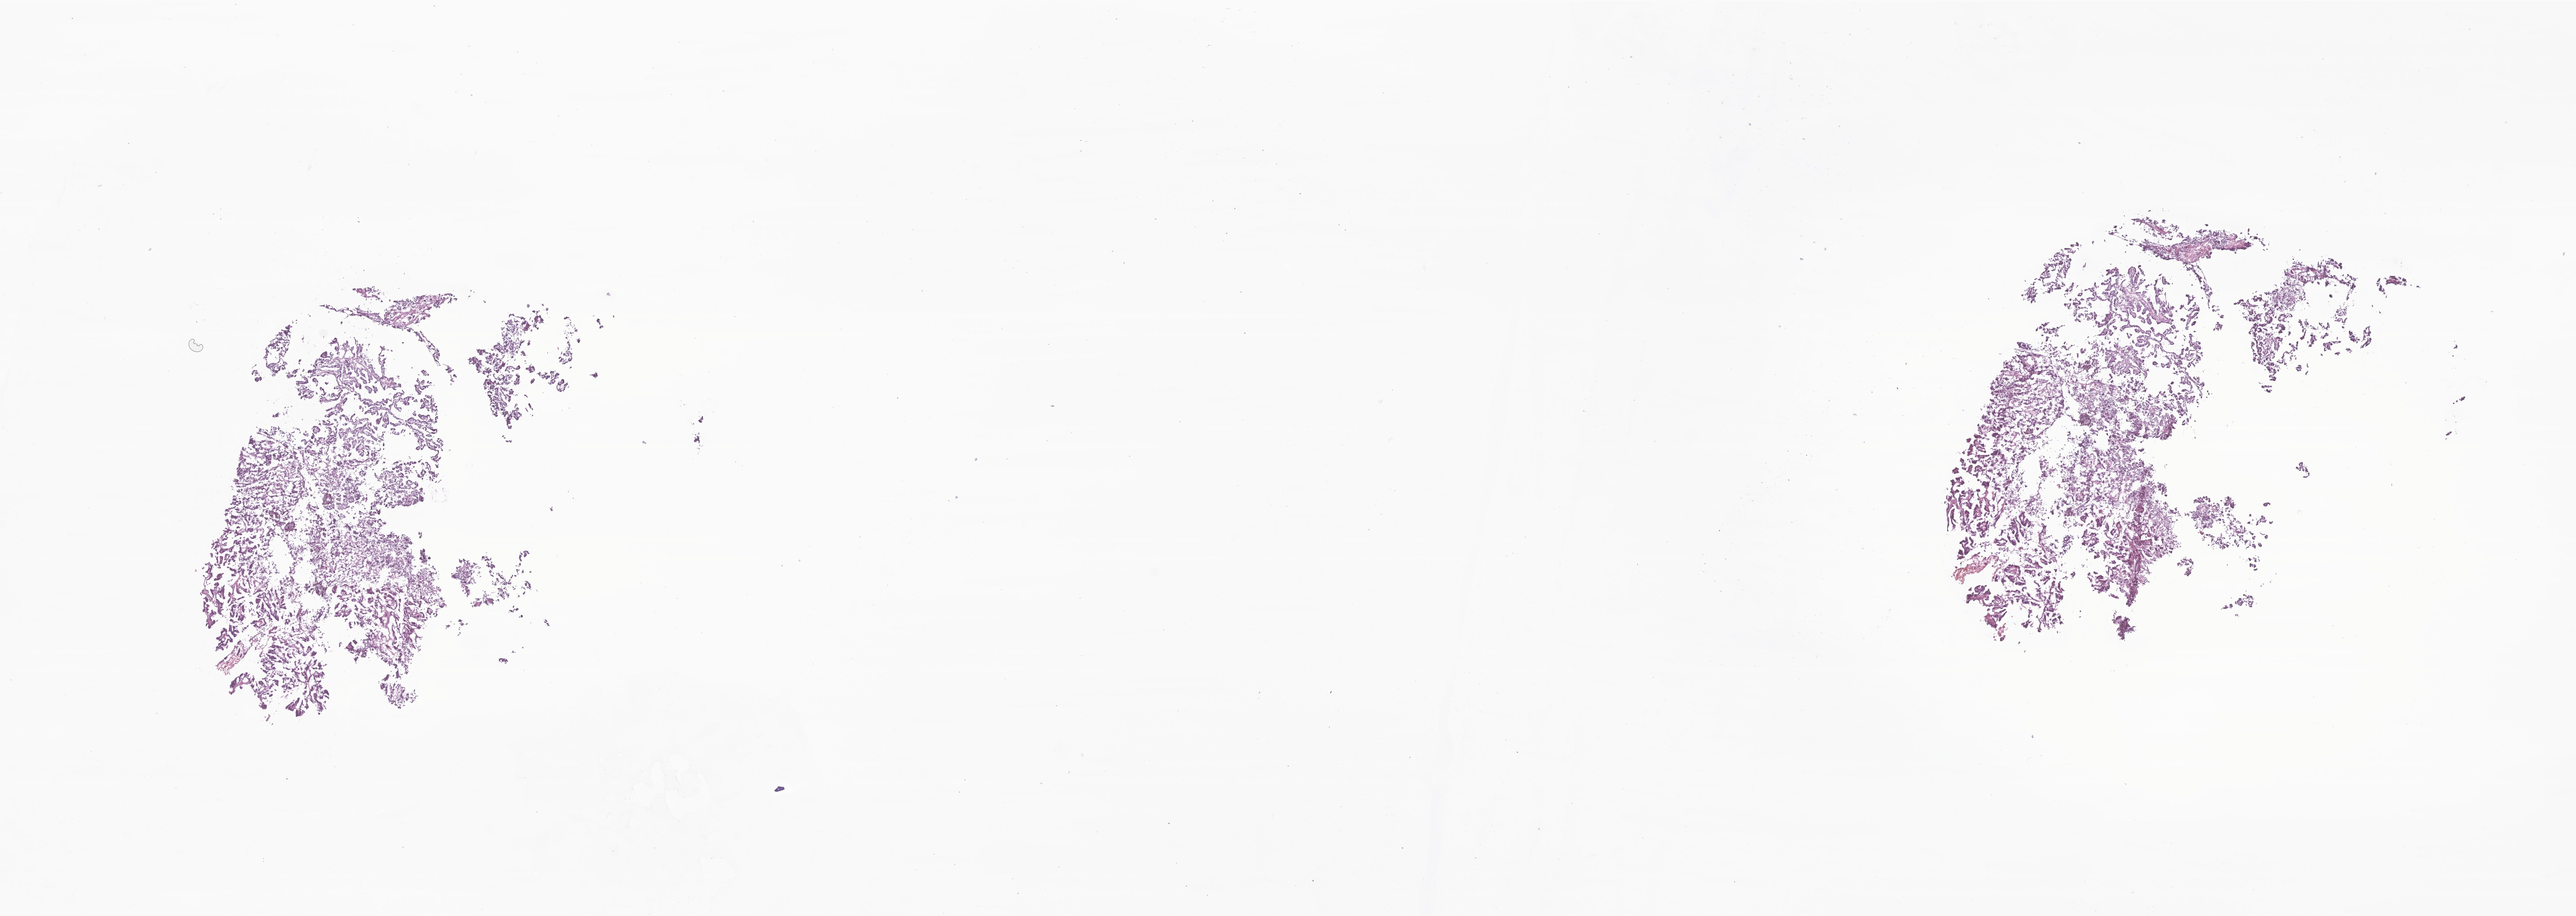
Digitized haematoxylin and eosin-stained section of tumor tissue from the brain, shown as a low-resolution overview of the whole scanned area (about 24.6 x 8.8 mm), frozen section (OCT-embedded). Patient: male, age 52 months (4 years 4 months).
Recorded diagnosis: Choroid plexus papilloma, NOS.